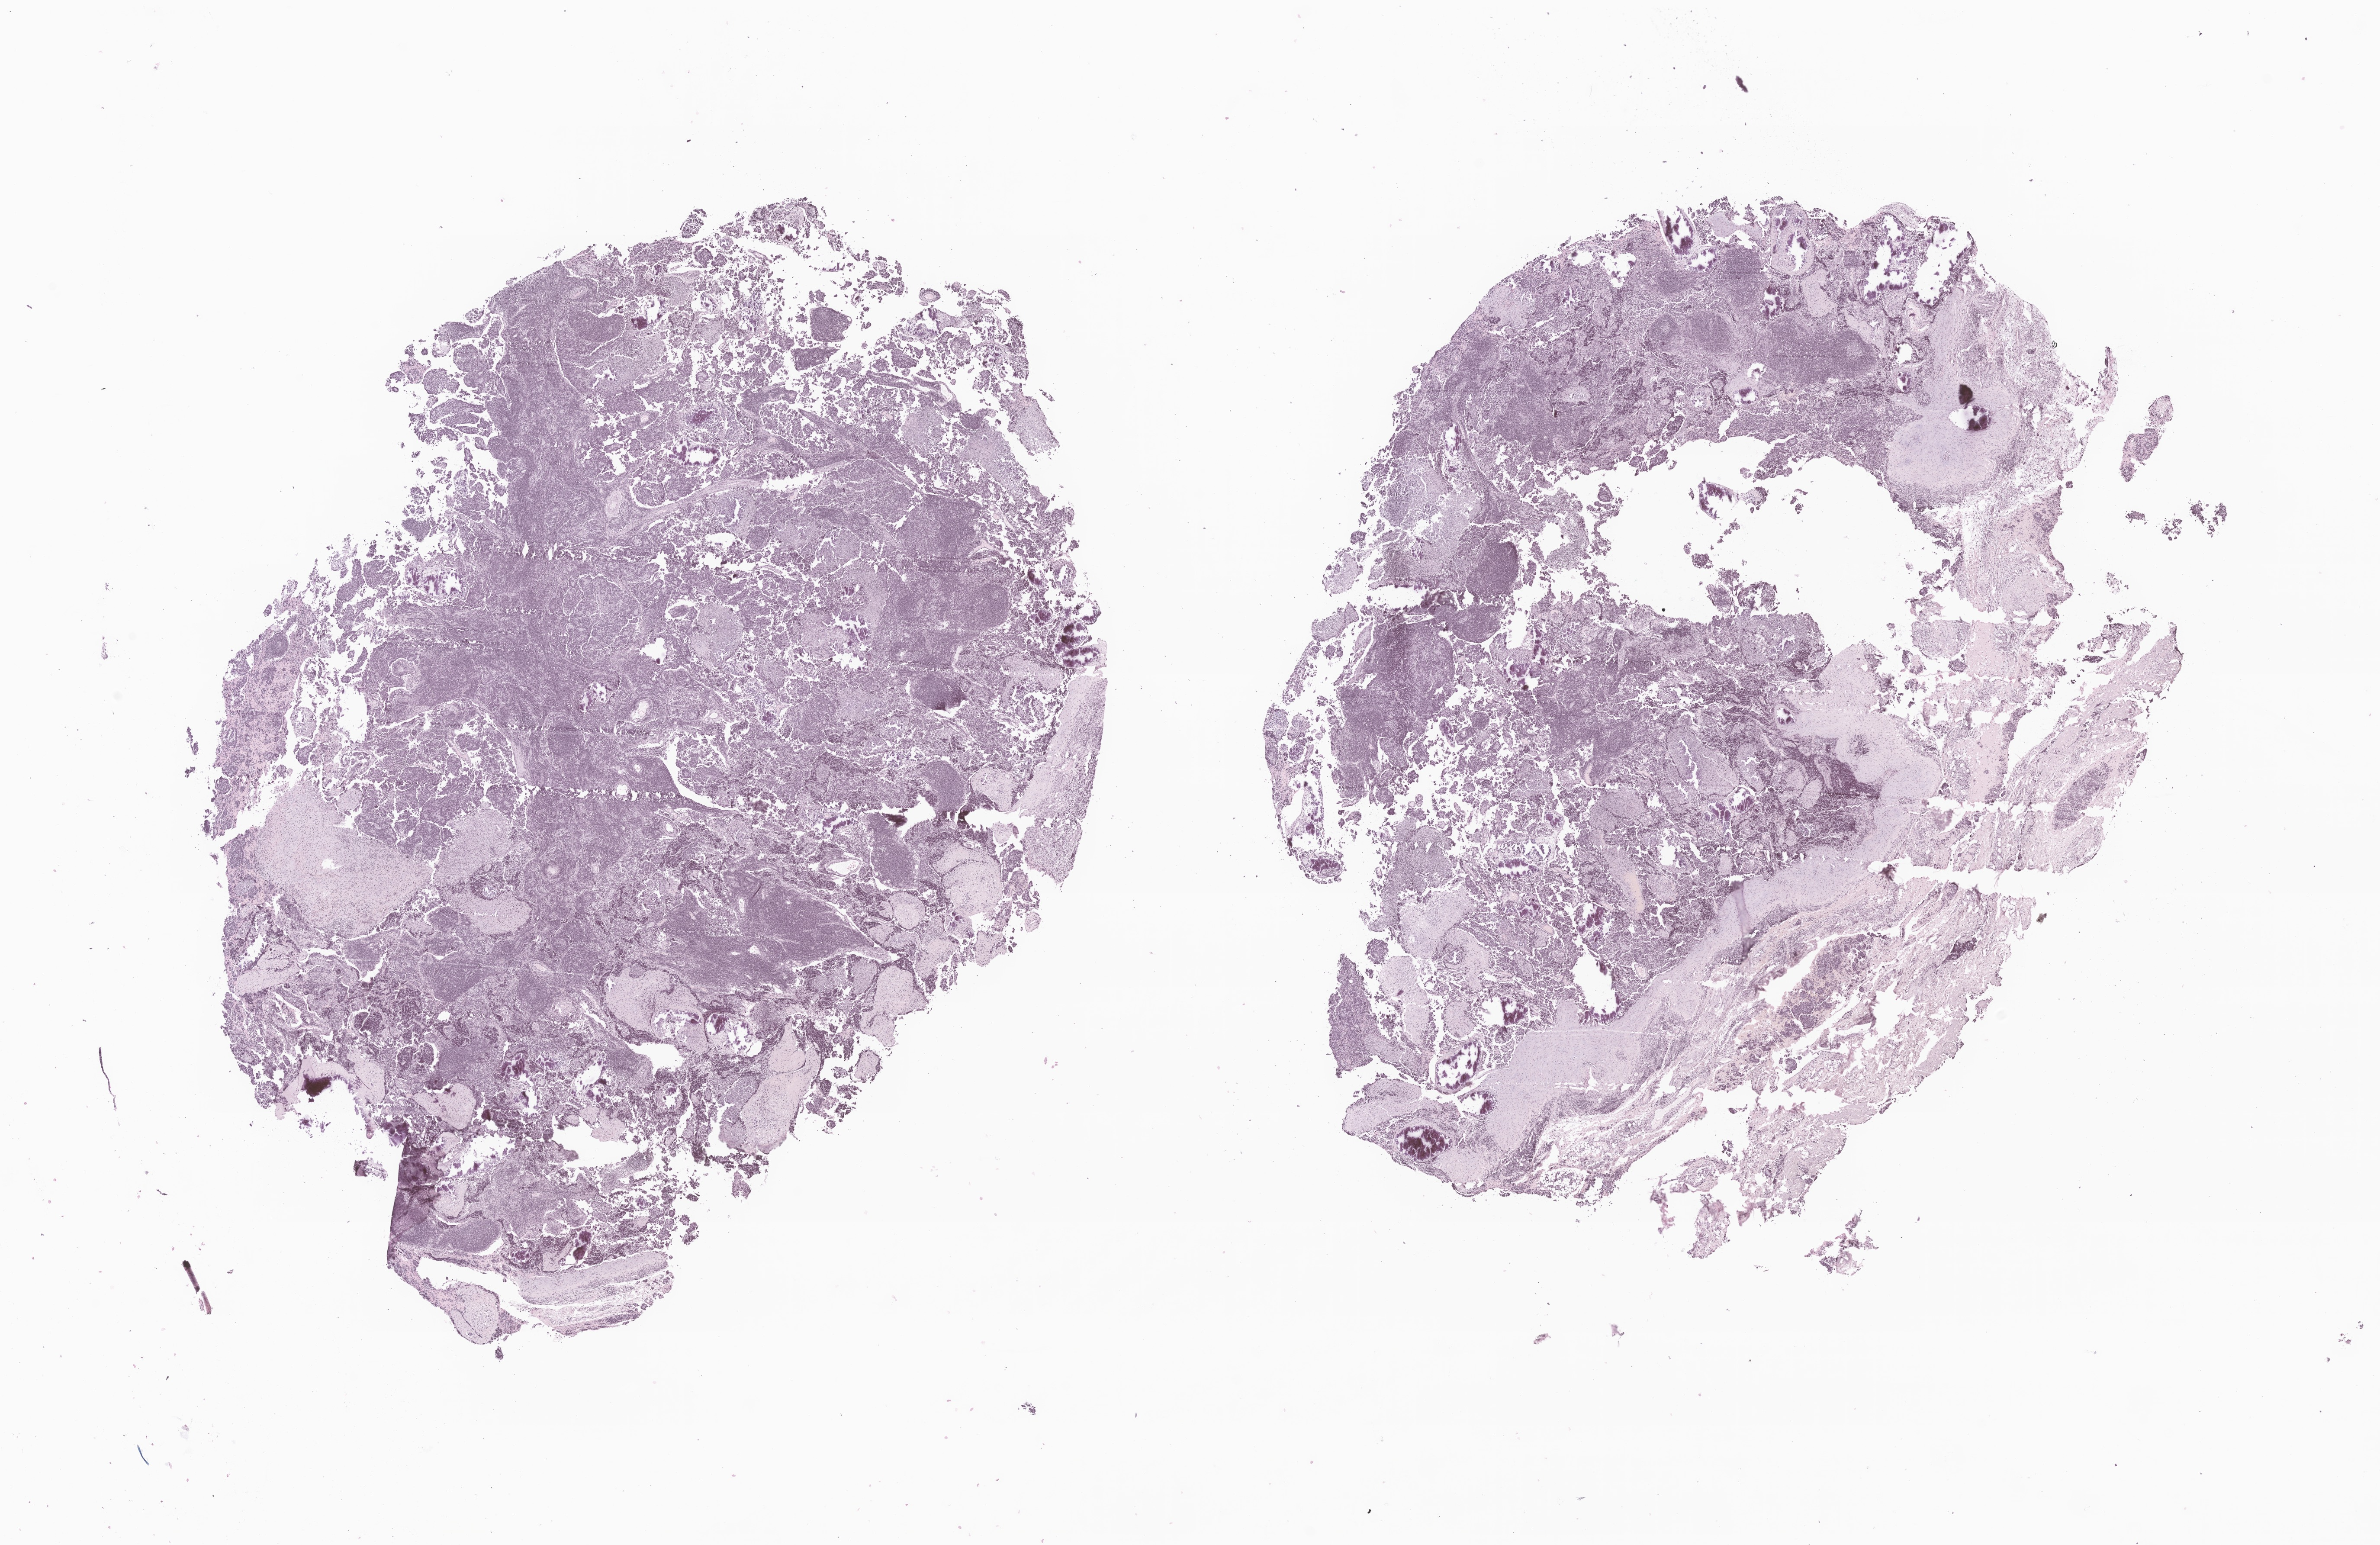
Digitized hematoxylin and eosin (H&E)-stained section of tumor tissue from the adrenal gland — low-resolution overview of the scanned area, about 23.2 x 15.0 mm. Formalin-fixed paraffin-embedded section. Patient male; age 39 months (3 years 3 months).
* recorded diagnosis: Neuroblastoma, NOS